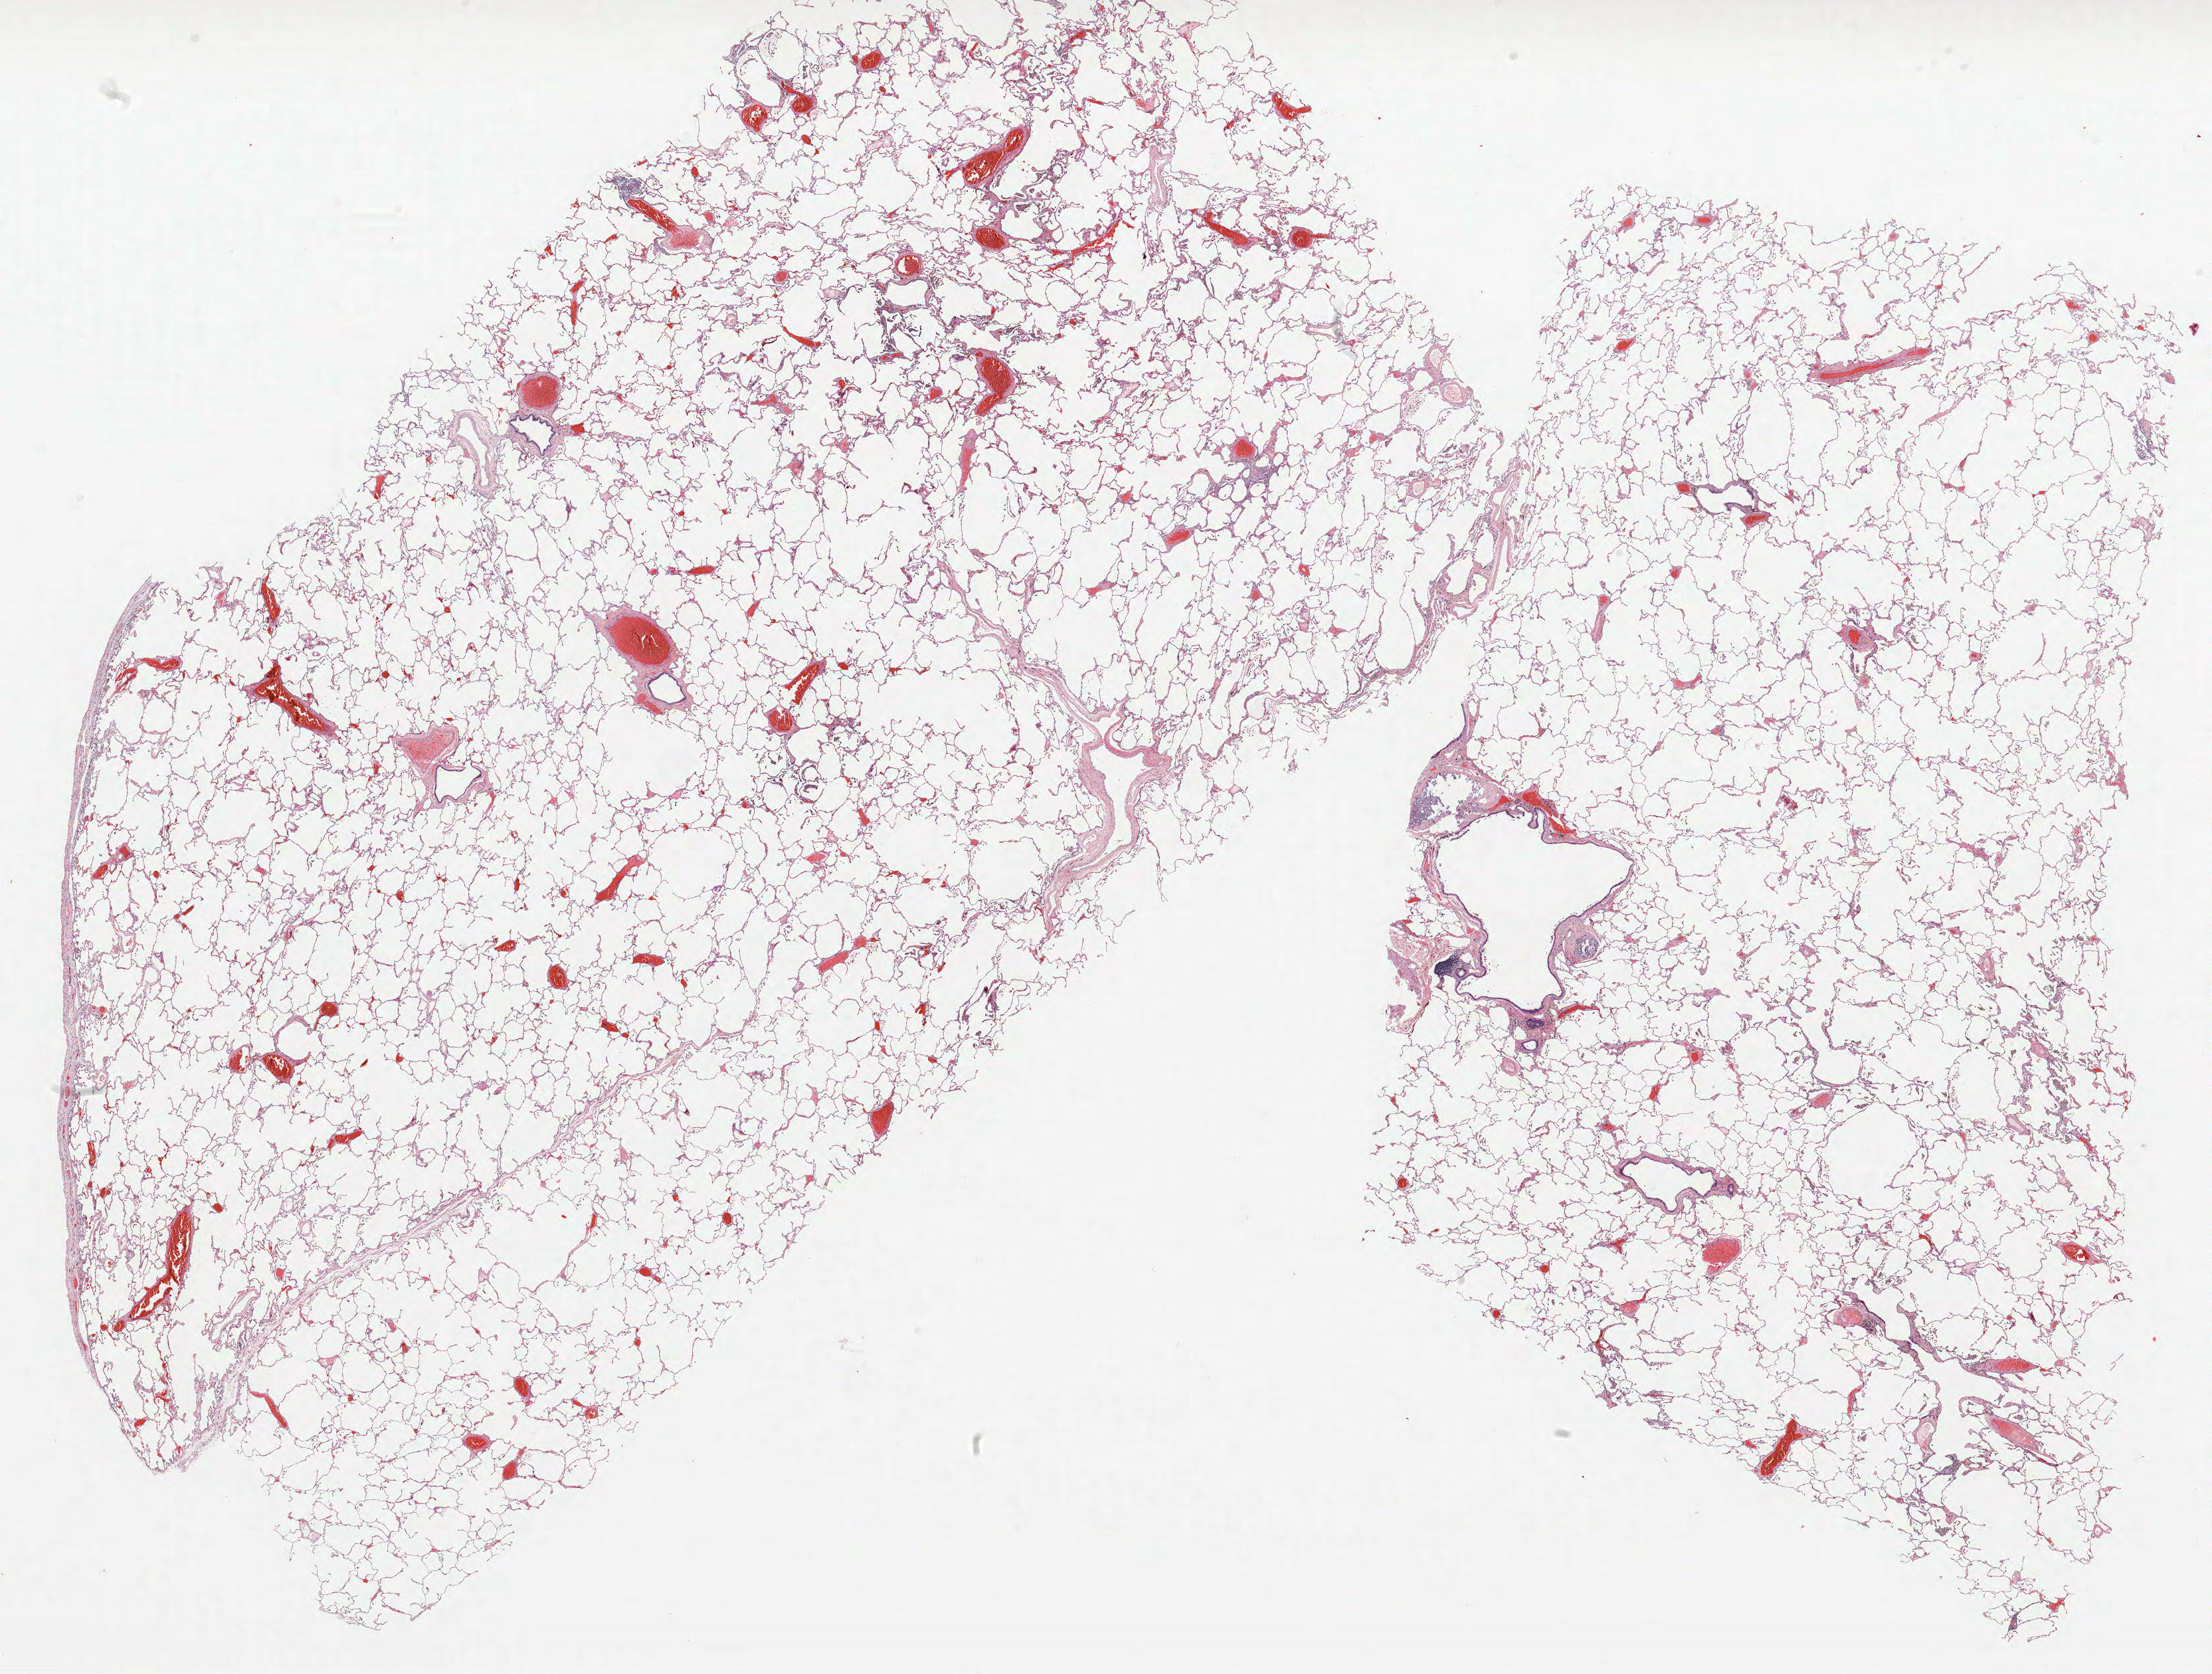
H&E-stained whole-slide image — a low-resolution overview of the entire scanned area, about 26.6 x 20.2 mm. FFPE section. Lung. Male patient, aged 57 at enrolment. Current smoker at enrolment. Grade: moderately differentiated (G2).
Participant's lung-cancer diagnosis: Squamous cell carcinoma, NOS (ICD-O-3 8070/3). Tumour size (pathology): 35 mm. Stage (AJCC 6th edition): IB. Primary tumour location (clinical record): left lower lobe.